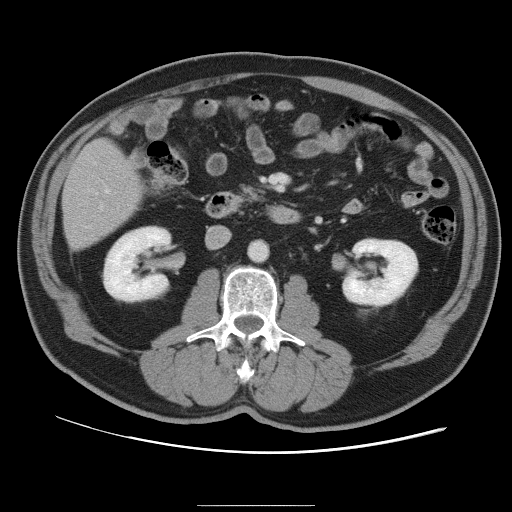
Contrast-enhanced abdominal CT, one axial slice; position 31 of 105 along the scan axis; intravenous contrast given; soft-tissue window (W 400 / L 40 HU); 5 mm slice thickness; 512 × 512 image matrix. Male patient, age 64 years. From the clinical record (not read from this slice): diagnosis: colorectal cancer liver metastases, imaged before liver resection.
Structures marked on this image (expert manual segmentation):
- hepatic veins: bounding box (x1, y1, x2, y2) in pixels: (105, 190, 110, 193)
- liver: (64, 141, 141, 248)
- planned liver remnant (the part of the liver to remain after resection): (64, 142, 141, 232)